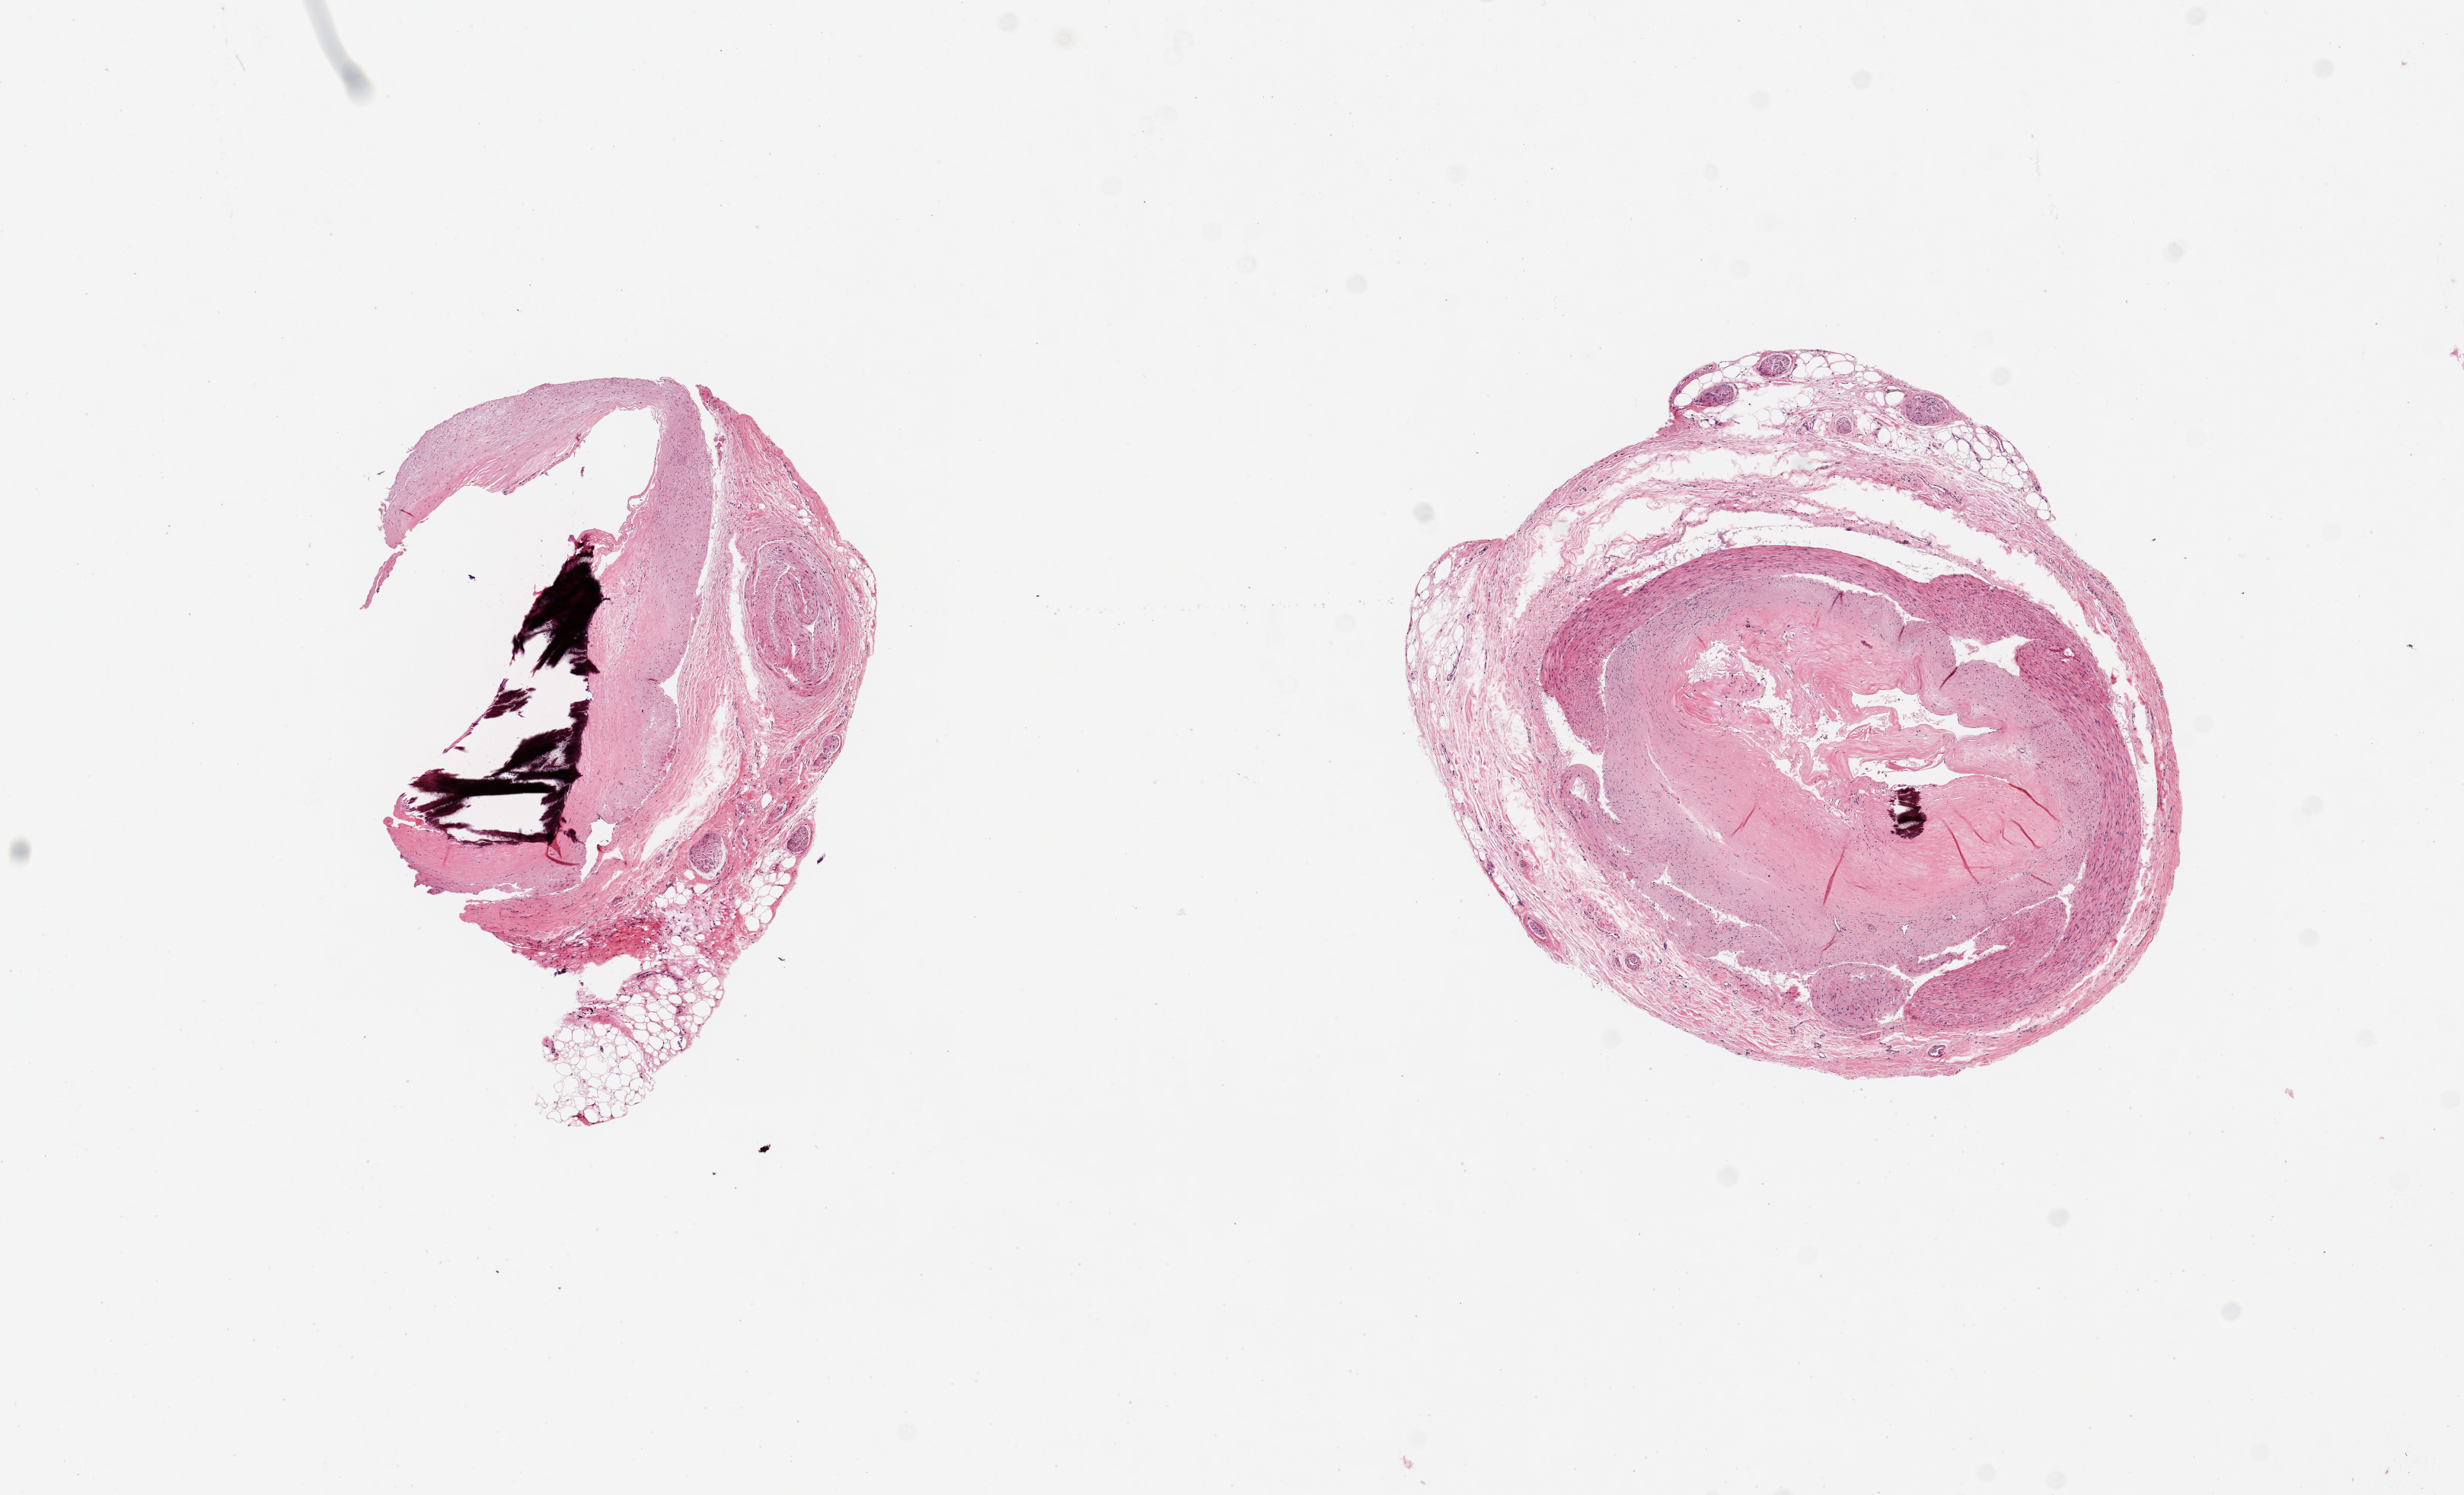
Whole-slide image, hematoxylin and eosin (H&E) stain, brightfield — whole scanned area (about 12.8 x 7.8 mm) shown as a low-resolution overview, PAXgene-fixed, paraffin-embedded tissue, target tissue: coronary artery, donor tissue sample. Donor sex: male.
- reviewer comment on this tissue sample: 2 pieces; severe calcific atherosclerosis with narrowing of the lumen (>75%), surrounding adventitia and external fat with nerves measures up to 1mm